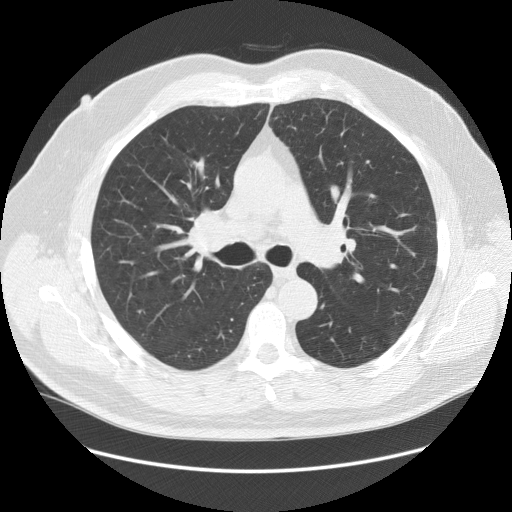
Chest CT (low-dose screening protocol), one axial image. First (baseline) screen. Lung window (W 1500 / L -600 HU). 2.5 mm slice thickness. Standard (soft-tissue) reconstruction kernel (STANDARD). Slice 52 of 140 in the series. 512 × 512 image matrix. Male, age 64 years at enrolment.
Expert reader's lesion annotation, bounding box (x1, y1, x2, y2) in pixels: (179, 202, 249, 271). The exam's reader record, not a measurement of the box and not confirmed to be the same lesion: non-calcified nodule or mass ≥4 mm, right lower lobe, 7 × 5 mm, smooth margins, soft tissue attenuation. Official screen result: positive, change unspecified: nodule(s) >= 4 mm or enlarging nodule(s), mass(es), or other non-specific abnormalities suspicious for lung cancer.